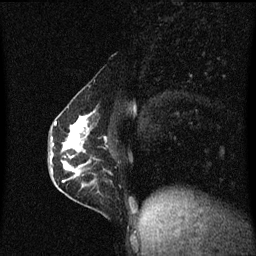
Breast MRI (dynamic contrast-enhanced), one sagittal slice; position 25 of 60 along the scan axis; dynamic contrast-enhanced series, image 2 of 3 at this slice position (ordered by acquisition); 1.5 T; TE 4.2 ms, TR 8.4 ms; 2 mm slice thickness; 256 × 256 image matrix, field of view 200 × 200 mm. Female patient, age 40 years.
Outlined on this slice (semi-automatic segmentation, software-assisted and operator-edited):
- analysis volume of interest (the breast-tissue region the enhancement analysis was run in; not a lesion): box from (x=57, y=110) to (x=105, y=191) px
- tumour enhancement mask (voxels above the 70 % enhancement threshold inside the analysis volume of interest): (x=61, y=112)–(x=95, y=183)